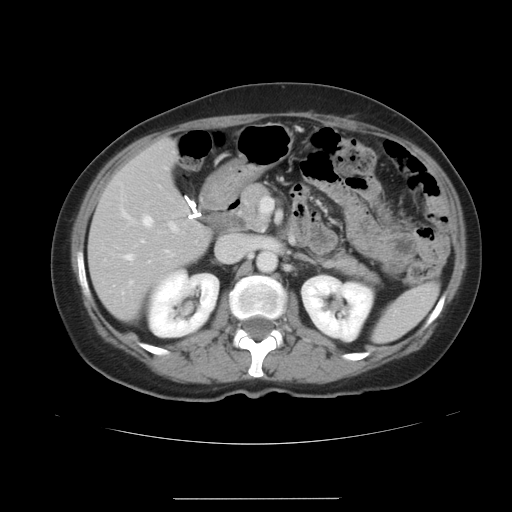
Contrast-enhanced abdominal CT, one axial slice; slice 19 of 41 in the series (ordered by position); intravenous contrast given; soft-tissue window (W 400 / L 40 HU); 5 mm slice thickness; 512 × 512 image matrix, field of view 381 × 381 mm. Female patient, age 63 years. From the clinical record (not read from this slice): diagnosis: colorectal cancer liver metastases, imaged before liver resection; multiple liver metastases: yes; largest metastasis: 1.5 cm; chemotherapy before resection: no.
Outlined on this slice (expert manual segmentation):
- hepatic veins: box from (x=123, y=212) to (x=153, y=259) px
- liver: (x=89, y=139)–(x=210, y=319)
- planned liver remnant (the part of the liver to remain after resection): (x=89, y=139)–(x=210, y=319)
- portal vein (with intrahepatic branches): (x=129, y=224)–(x=176, y=284)